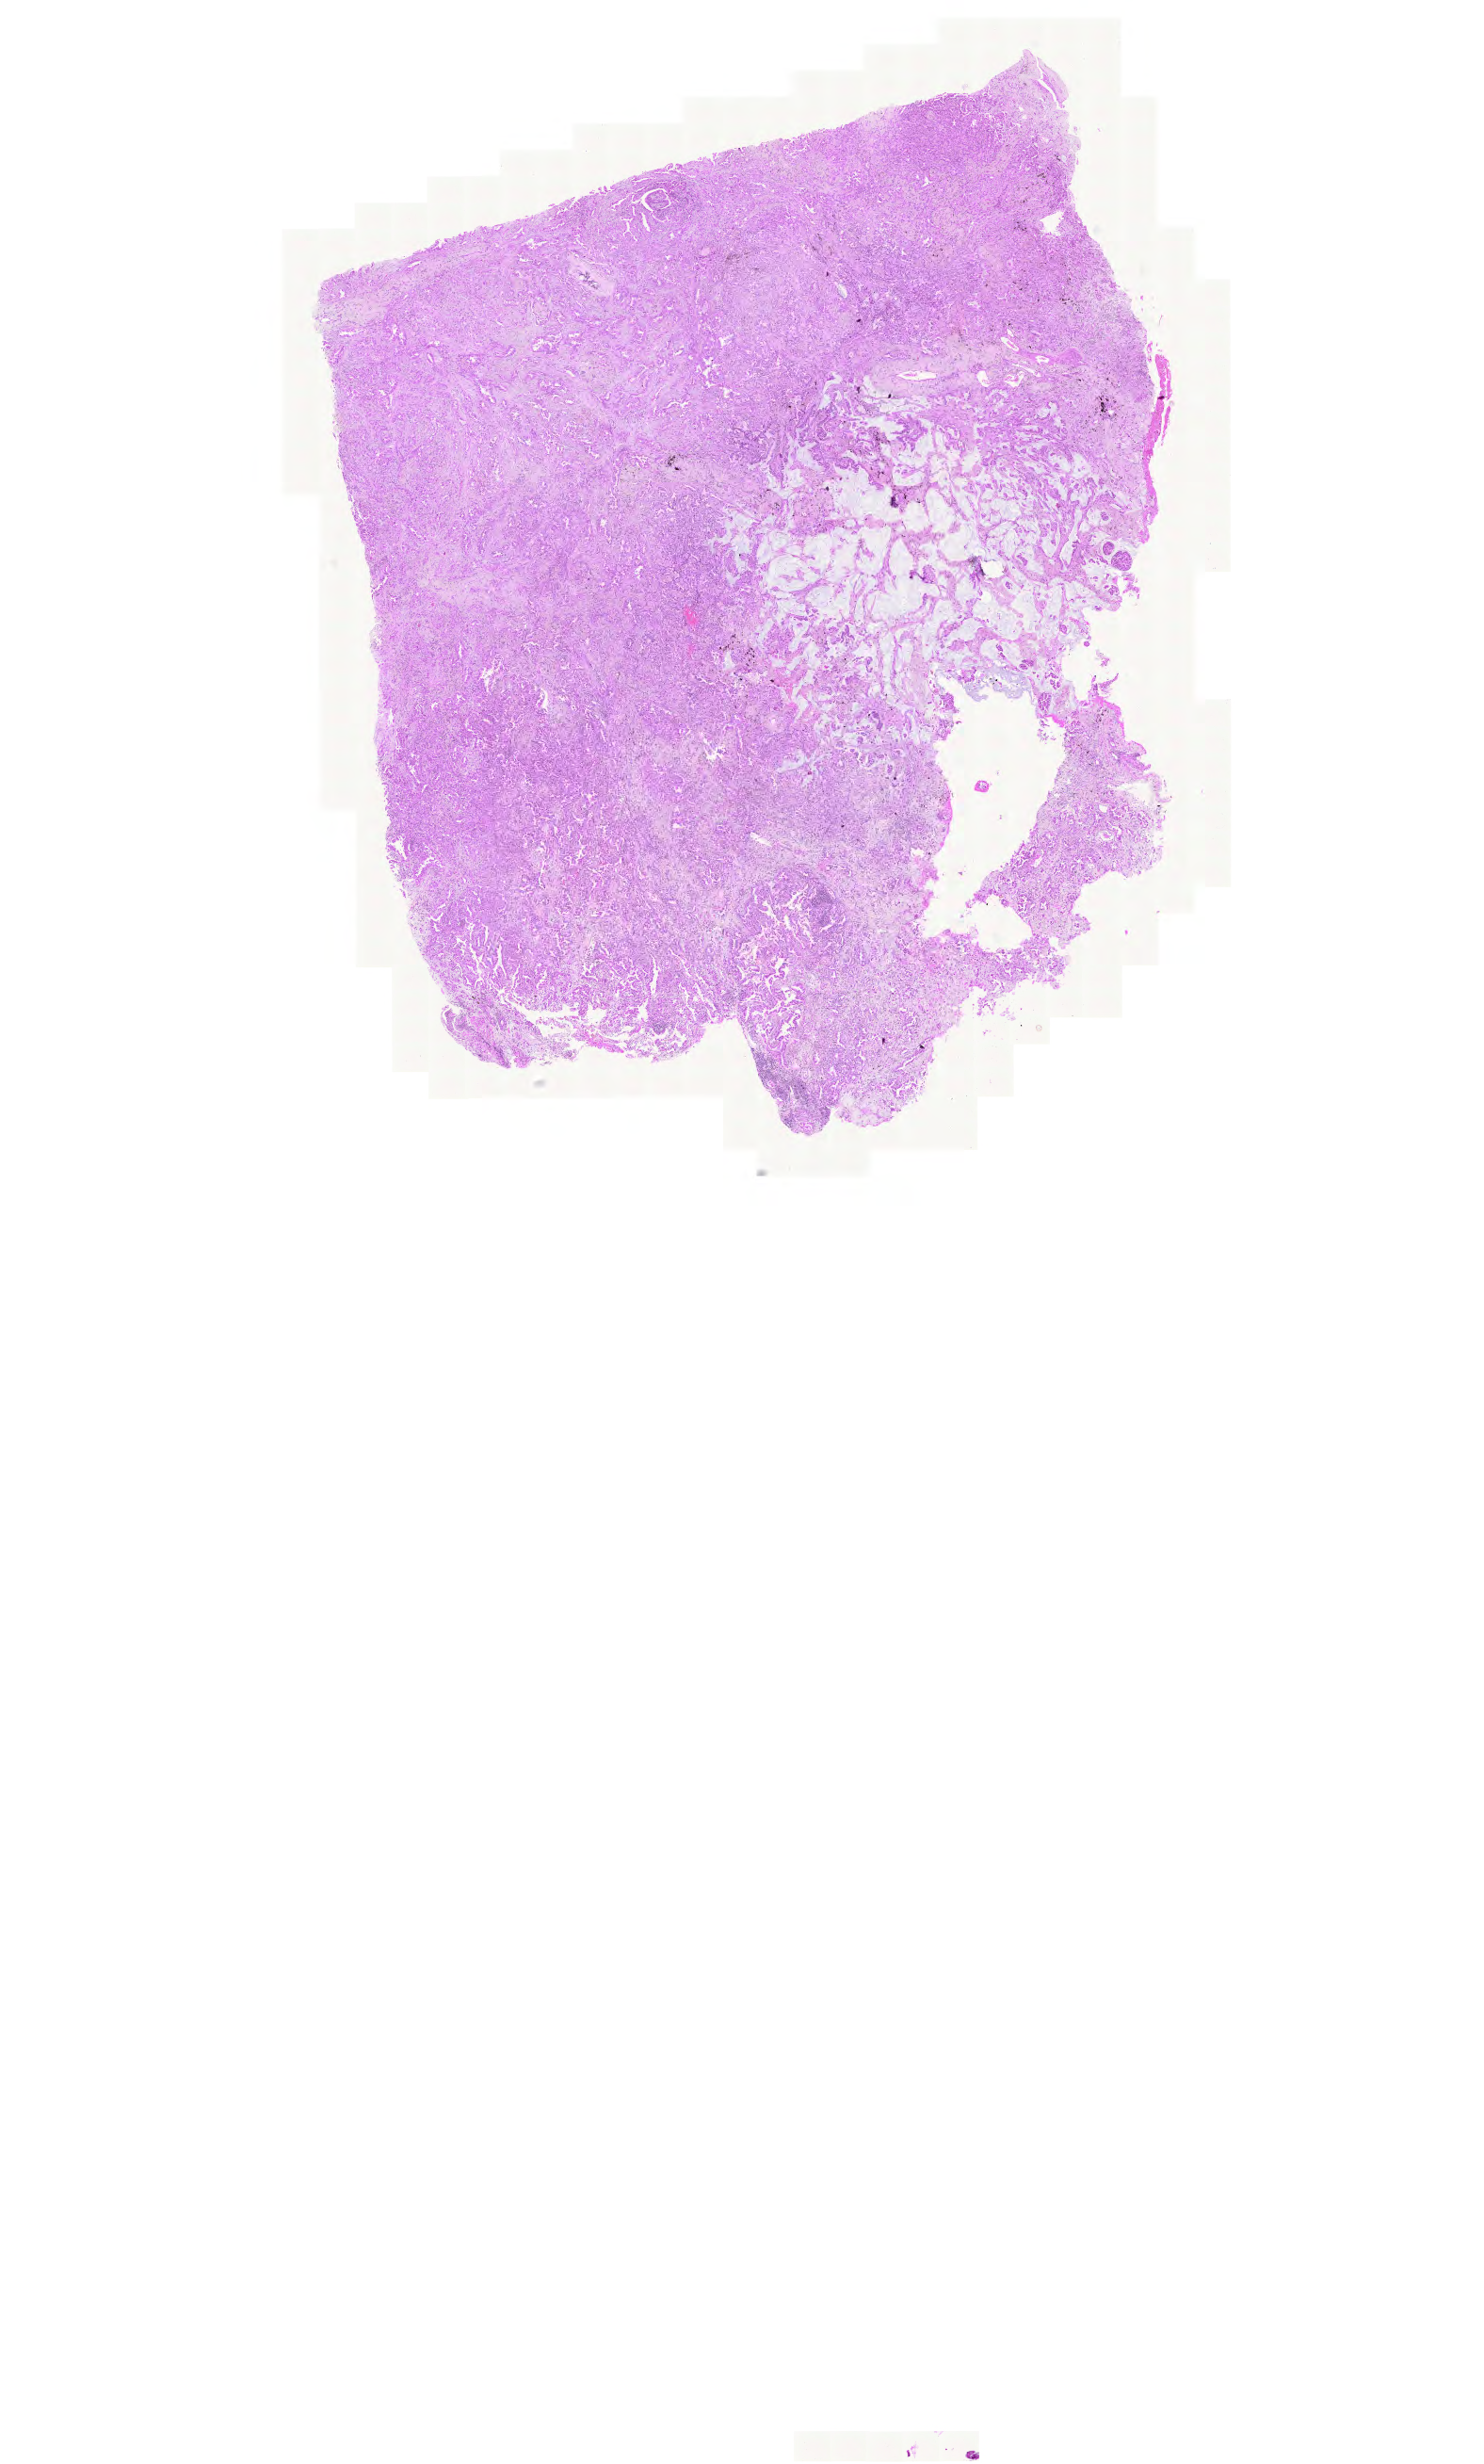
Whole-slide histology image, Hematoxylin and eosin (H&E) stained — shown as a low-resolution overview of the whole scanned area (about 11.7 x 19.5 mm, acquisition: 20x scan), formalin-fixed paraffin-embedded (FFPE) diagnostic section, sample: primary tumour, lung. Female patient; age at initial diagnosis 74 years.
- laterality: right
- AJCC pathologic stage: IB (5th edition)
- diagnosis: Adenocarcinoma with mixed subtypes (lower lobe, lung)